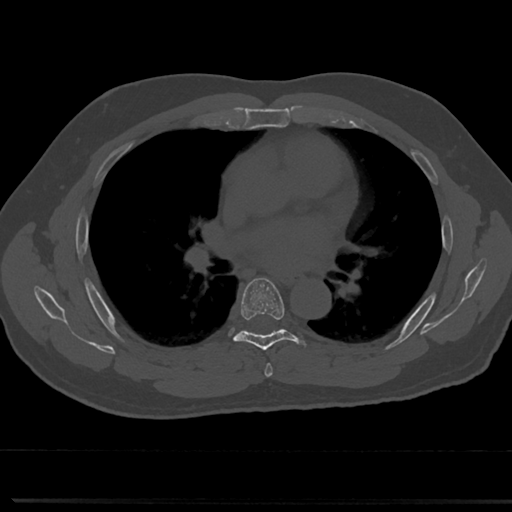
CT including the spine, one axial slice; position 453 of 817 along the scan axis; 120 kVp; bone window (W 1800 / L 400 HU); 0.5 mm slice thickness; 512 × 512 image matrix, field of view 355 × 355 mm. Male patient, age 61 years. Case-level facts recorded for this patient, not image findings: primary cancer: prostate.
Annotated regions visible in this slice (semi-automatically segmented with operator editing):
- T5 vertebra: bounding box [x1, y1, x2, y2] px = [262, 346, 273, 374]
- T6 vertebra: [218, 276, 310, 355]